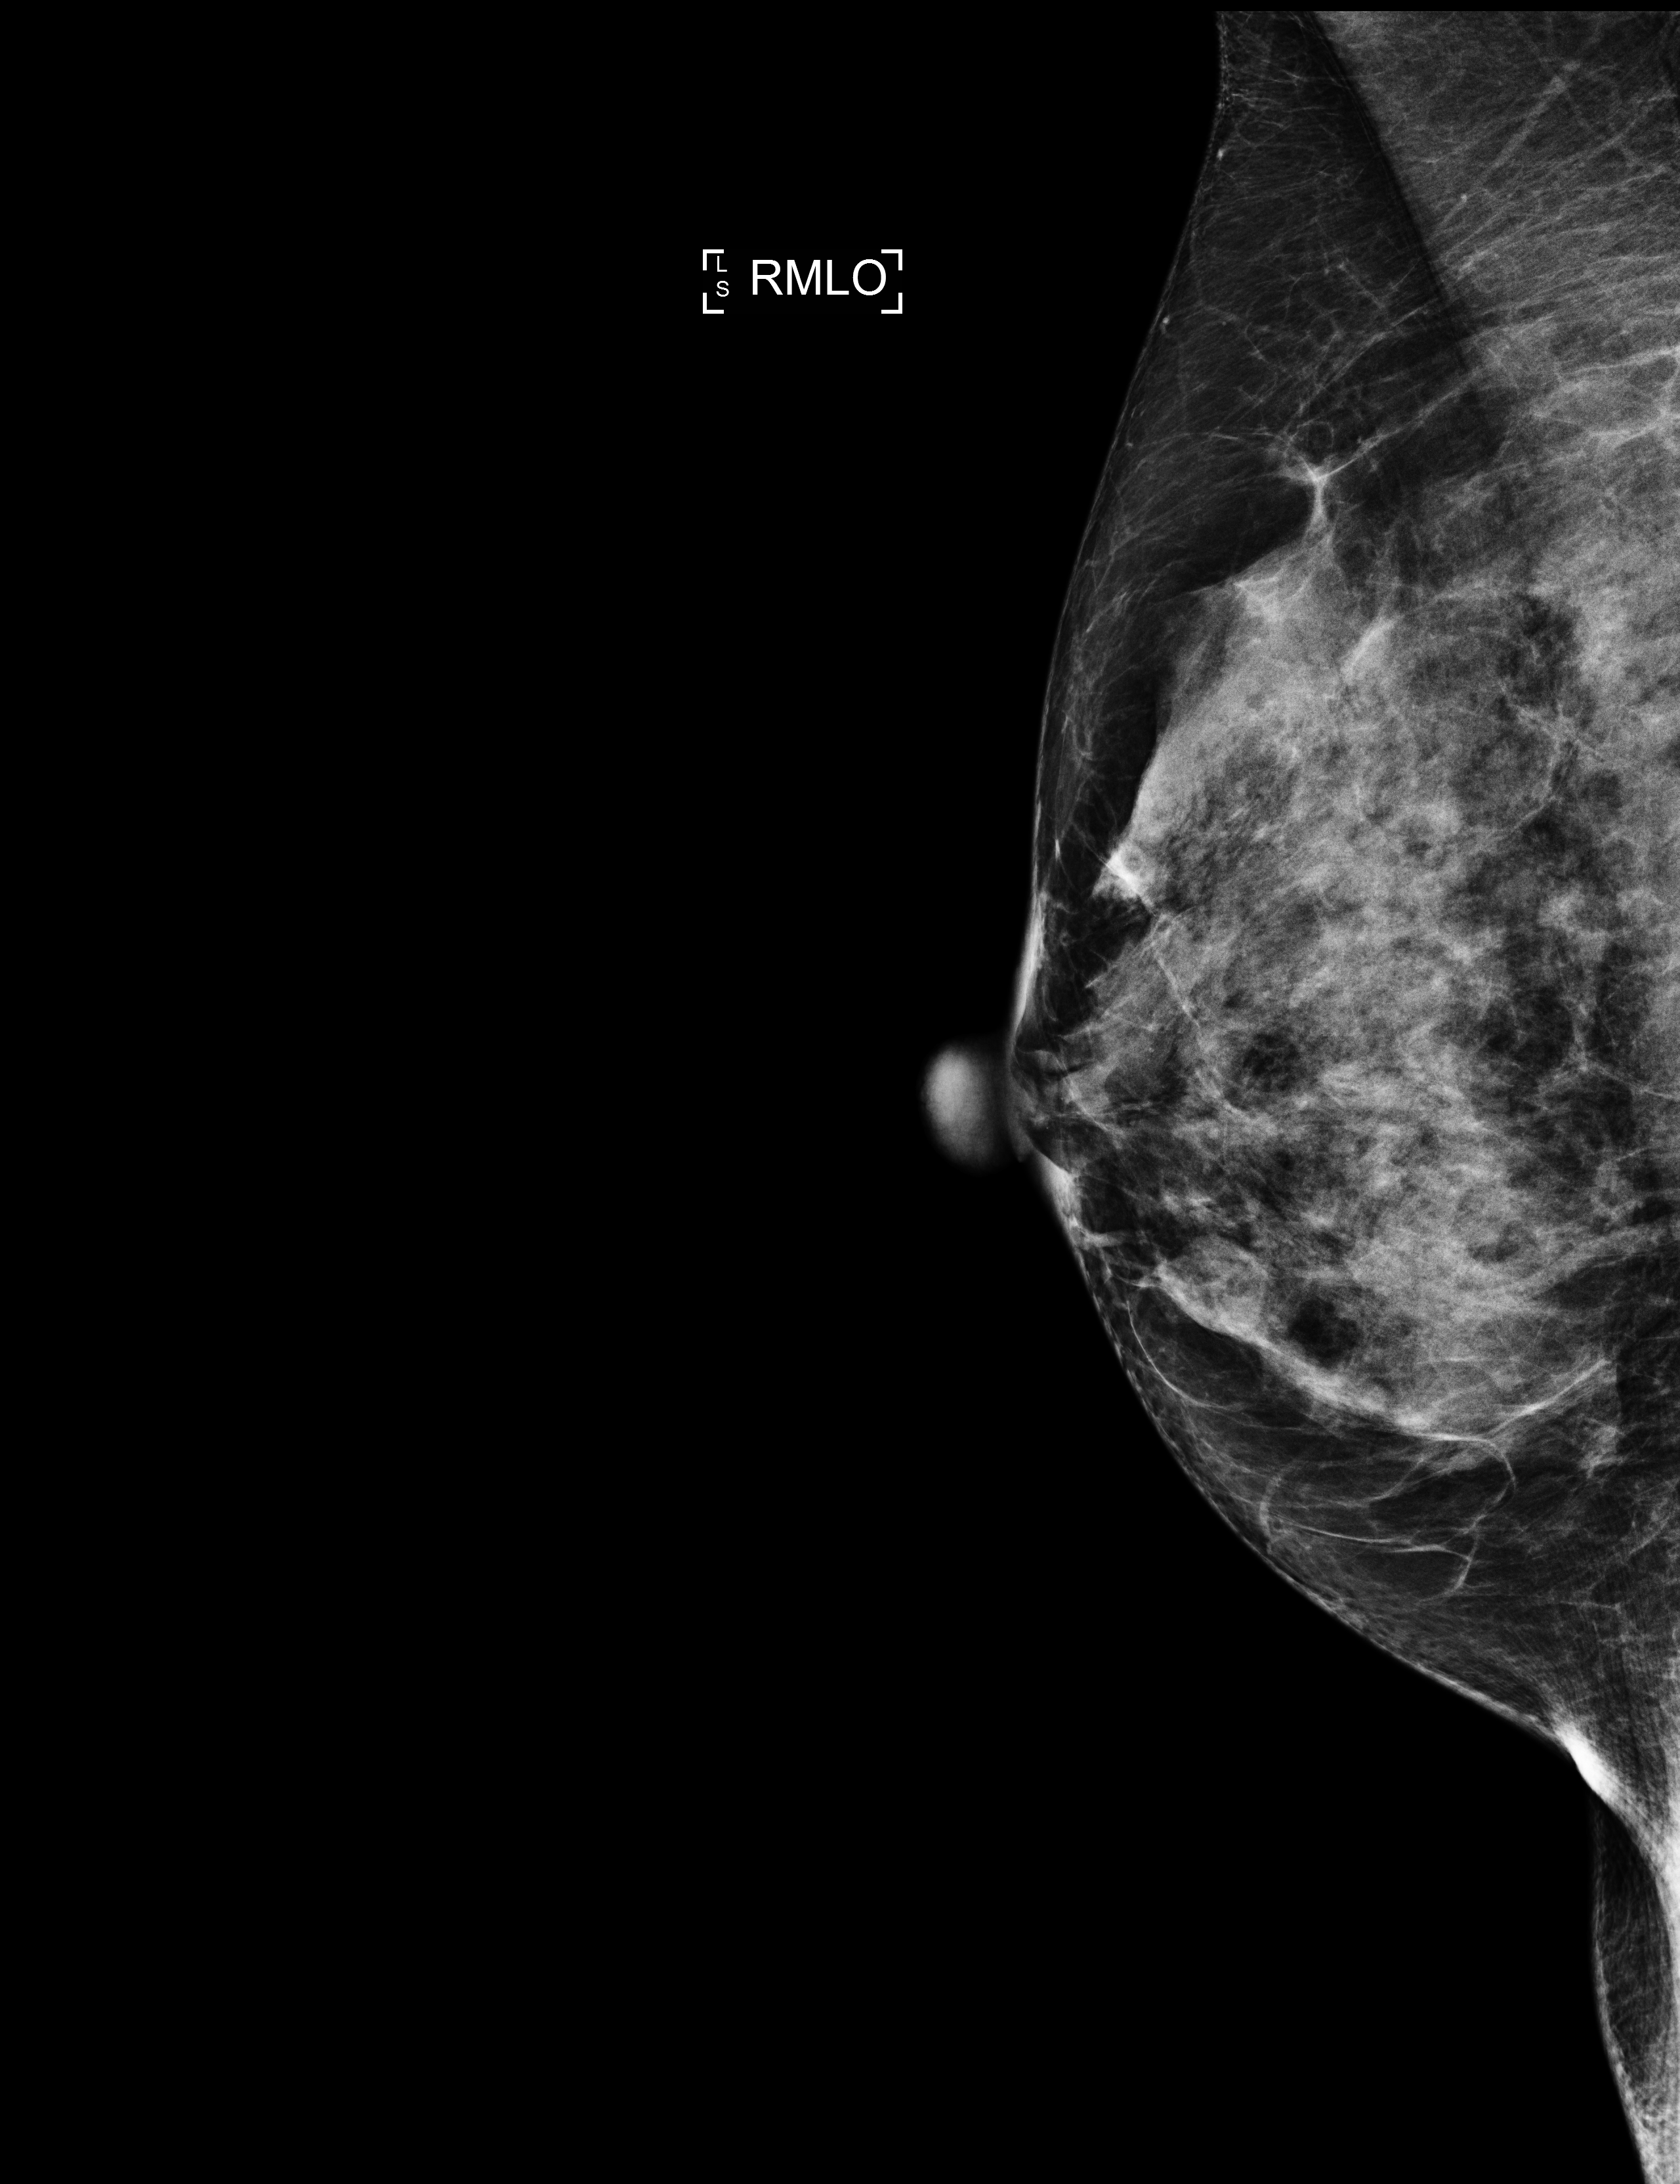
Digital mammogram (FFDM), right breast, MLO view, screening examination. Patient: female, 67 years.
BI-RADS breast density category at the screening exam (both breasts, scale 1–4): 4. Final BI-RADS category for the screening round (tomosynthesis exam, both breasts): category 2. Recall: no recall after this screen.